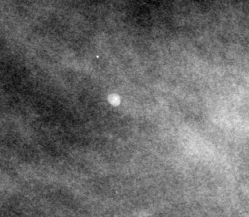
Cropped region of a digitized screen-film mammogram centred on a radiologist-marked abnormality; left breast; MLO view.
- Marked abnormality: calcifications, morphology punctate; BI-RADS assessment category 2; subtlety rating 3 on a 1 (subtle) to 5 (obvious) scale; benign; no additional work-up was recommended (benign without callback).